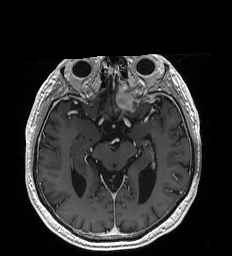
Brain MRI from a brain-tumour surgery series, one axial slice; slice 116 of 192 in the series (ordered by position); T1-weighted post-contrast; 1 mm slice thickness; 232 × 256 image matrix, field of view 227 × 250 mm. Case-level facts recorded for this patient, not image findings: histopathology: Glioblastoma; WHO grade: 4; IDH mutation: no.
Structures marked on this image (manually delineated by an expert):
- tumour: box from (x=116, y=87) to (x=134, y=110) px